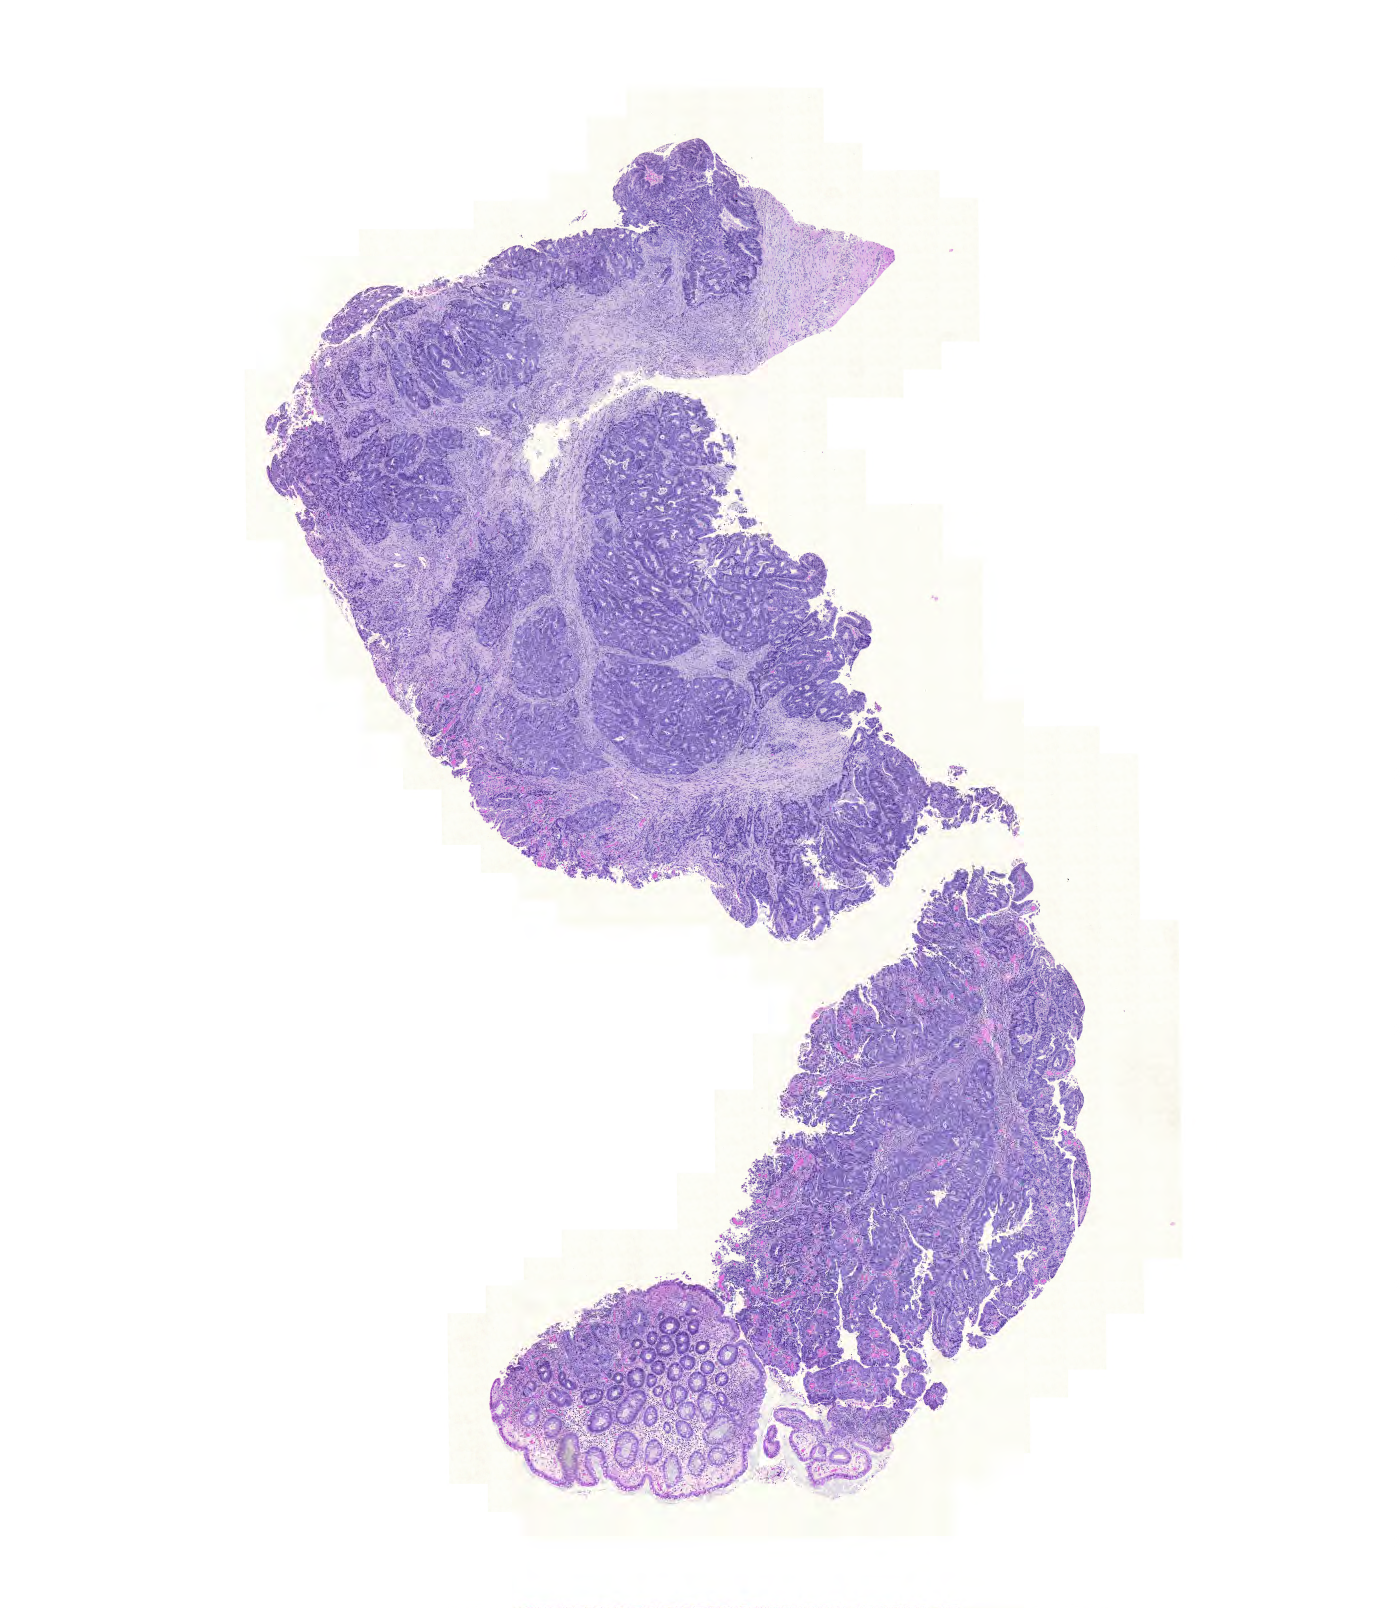
Digitized H&E tissue section (whole slide) — low-resolution overview of the scanned area, about 10.4 x 12.0 mm (slide scanned at 20x); FFPE section; rectum, primary tumour sample. Patient: female, age at initial diagnosis 79 years.
Pathologic diagnosis: Adenocarcinoma, NOS.